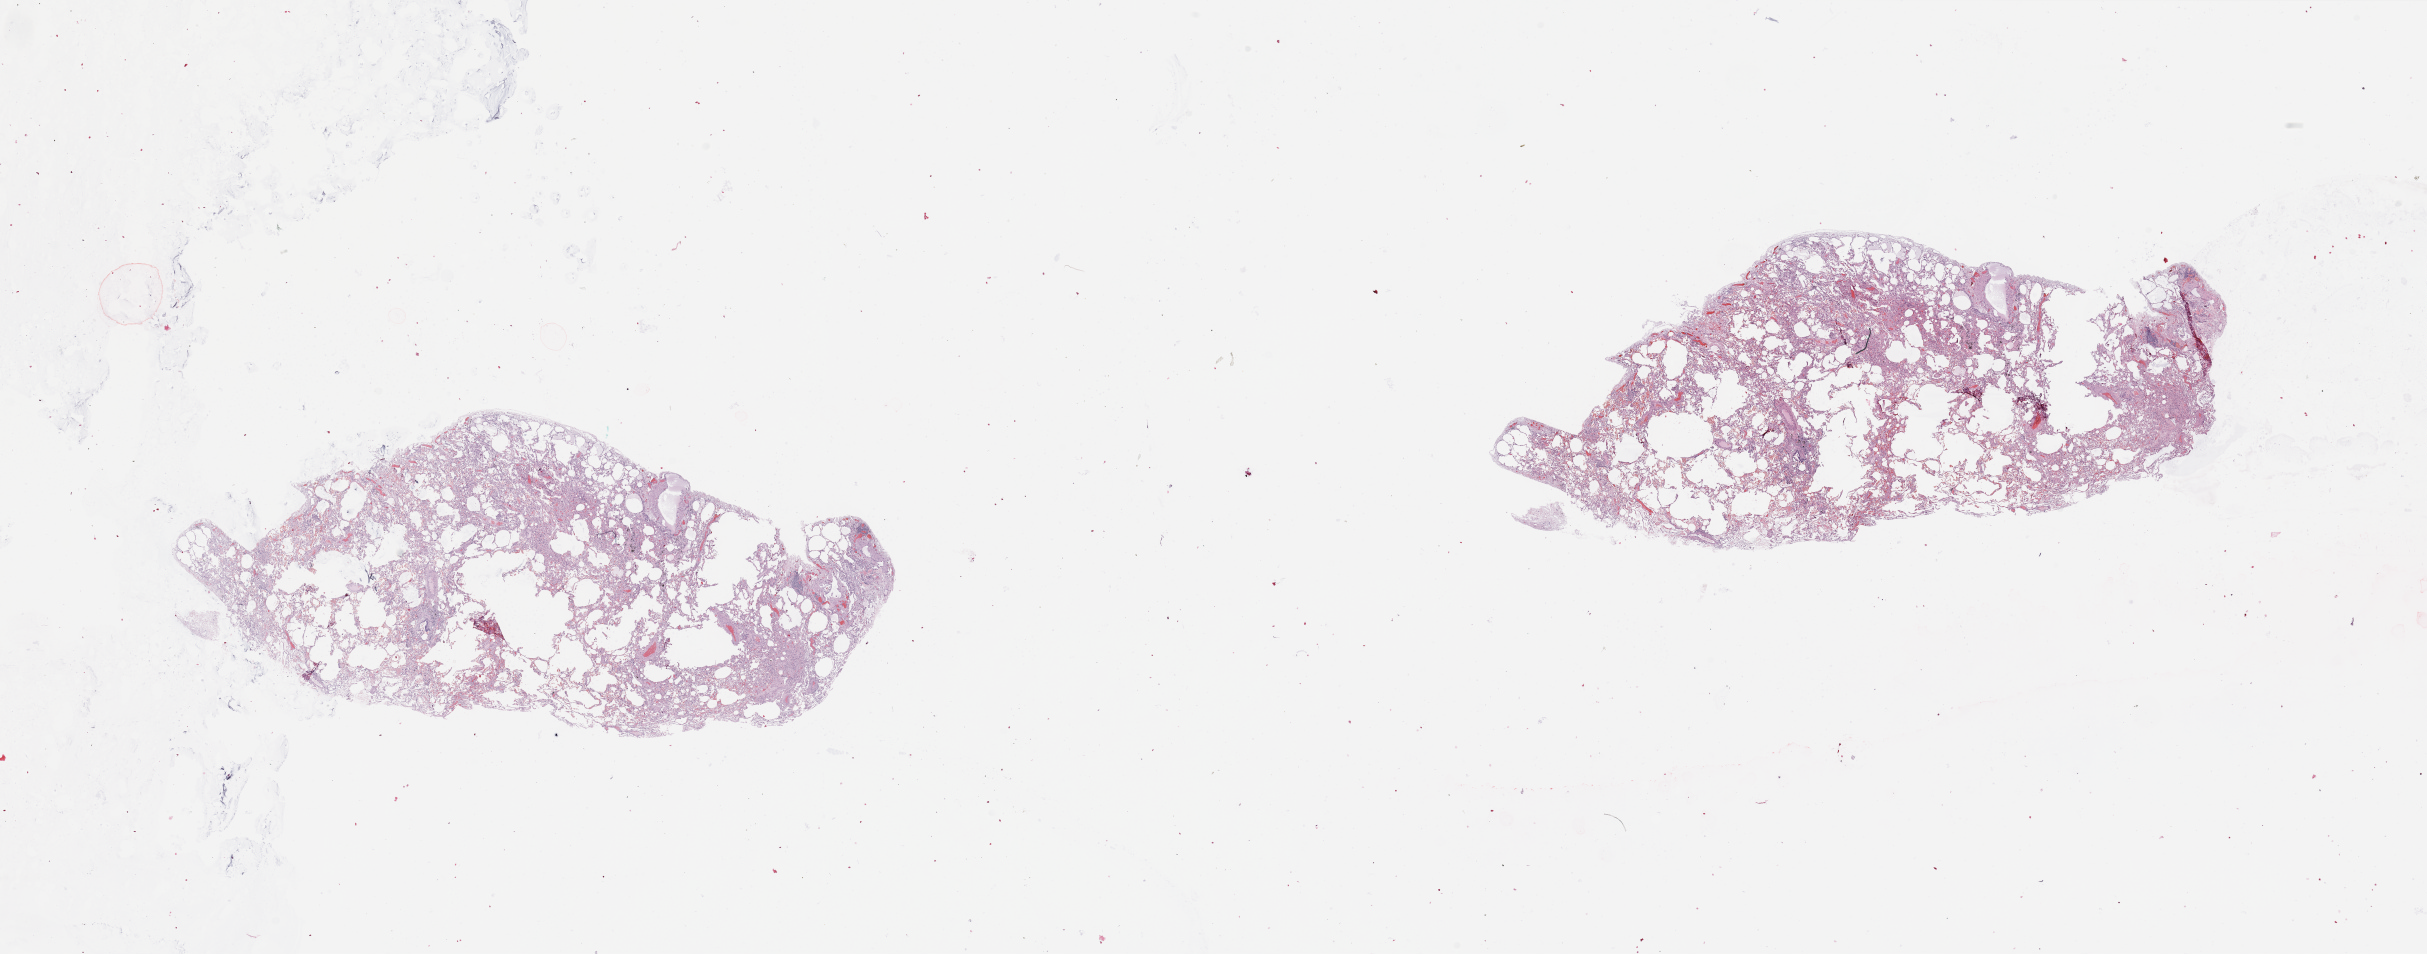
Digitized H&E tissue section (whole slide), whole scanned area (about 38.4 x 15.1 mm, from a 20x scan) shown as a low-resolution overview; normal (non-tumour) tissue sample, lung. 62-year-old male patient.
This section: normal (non-tumour) tissue from the same patient. Patient diagnosis: Squamous cell carcinoma, NOS.